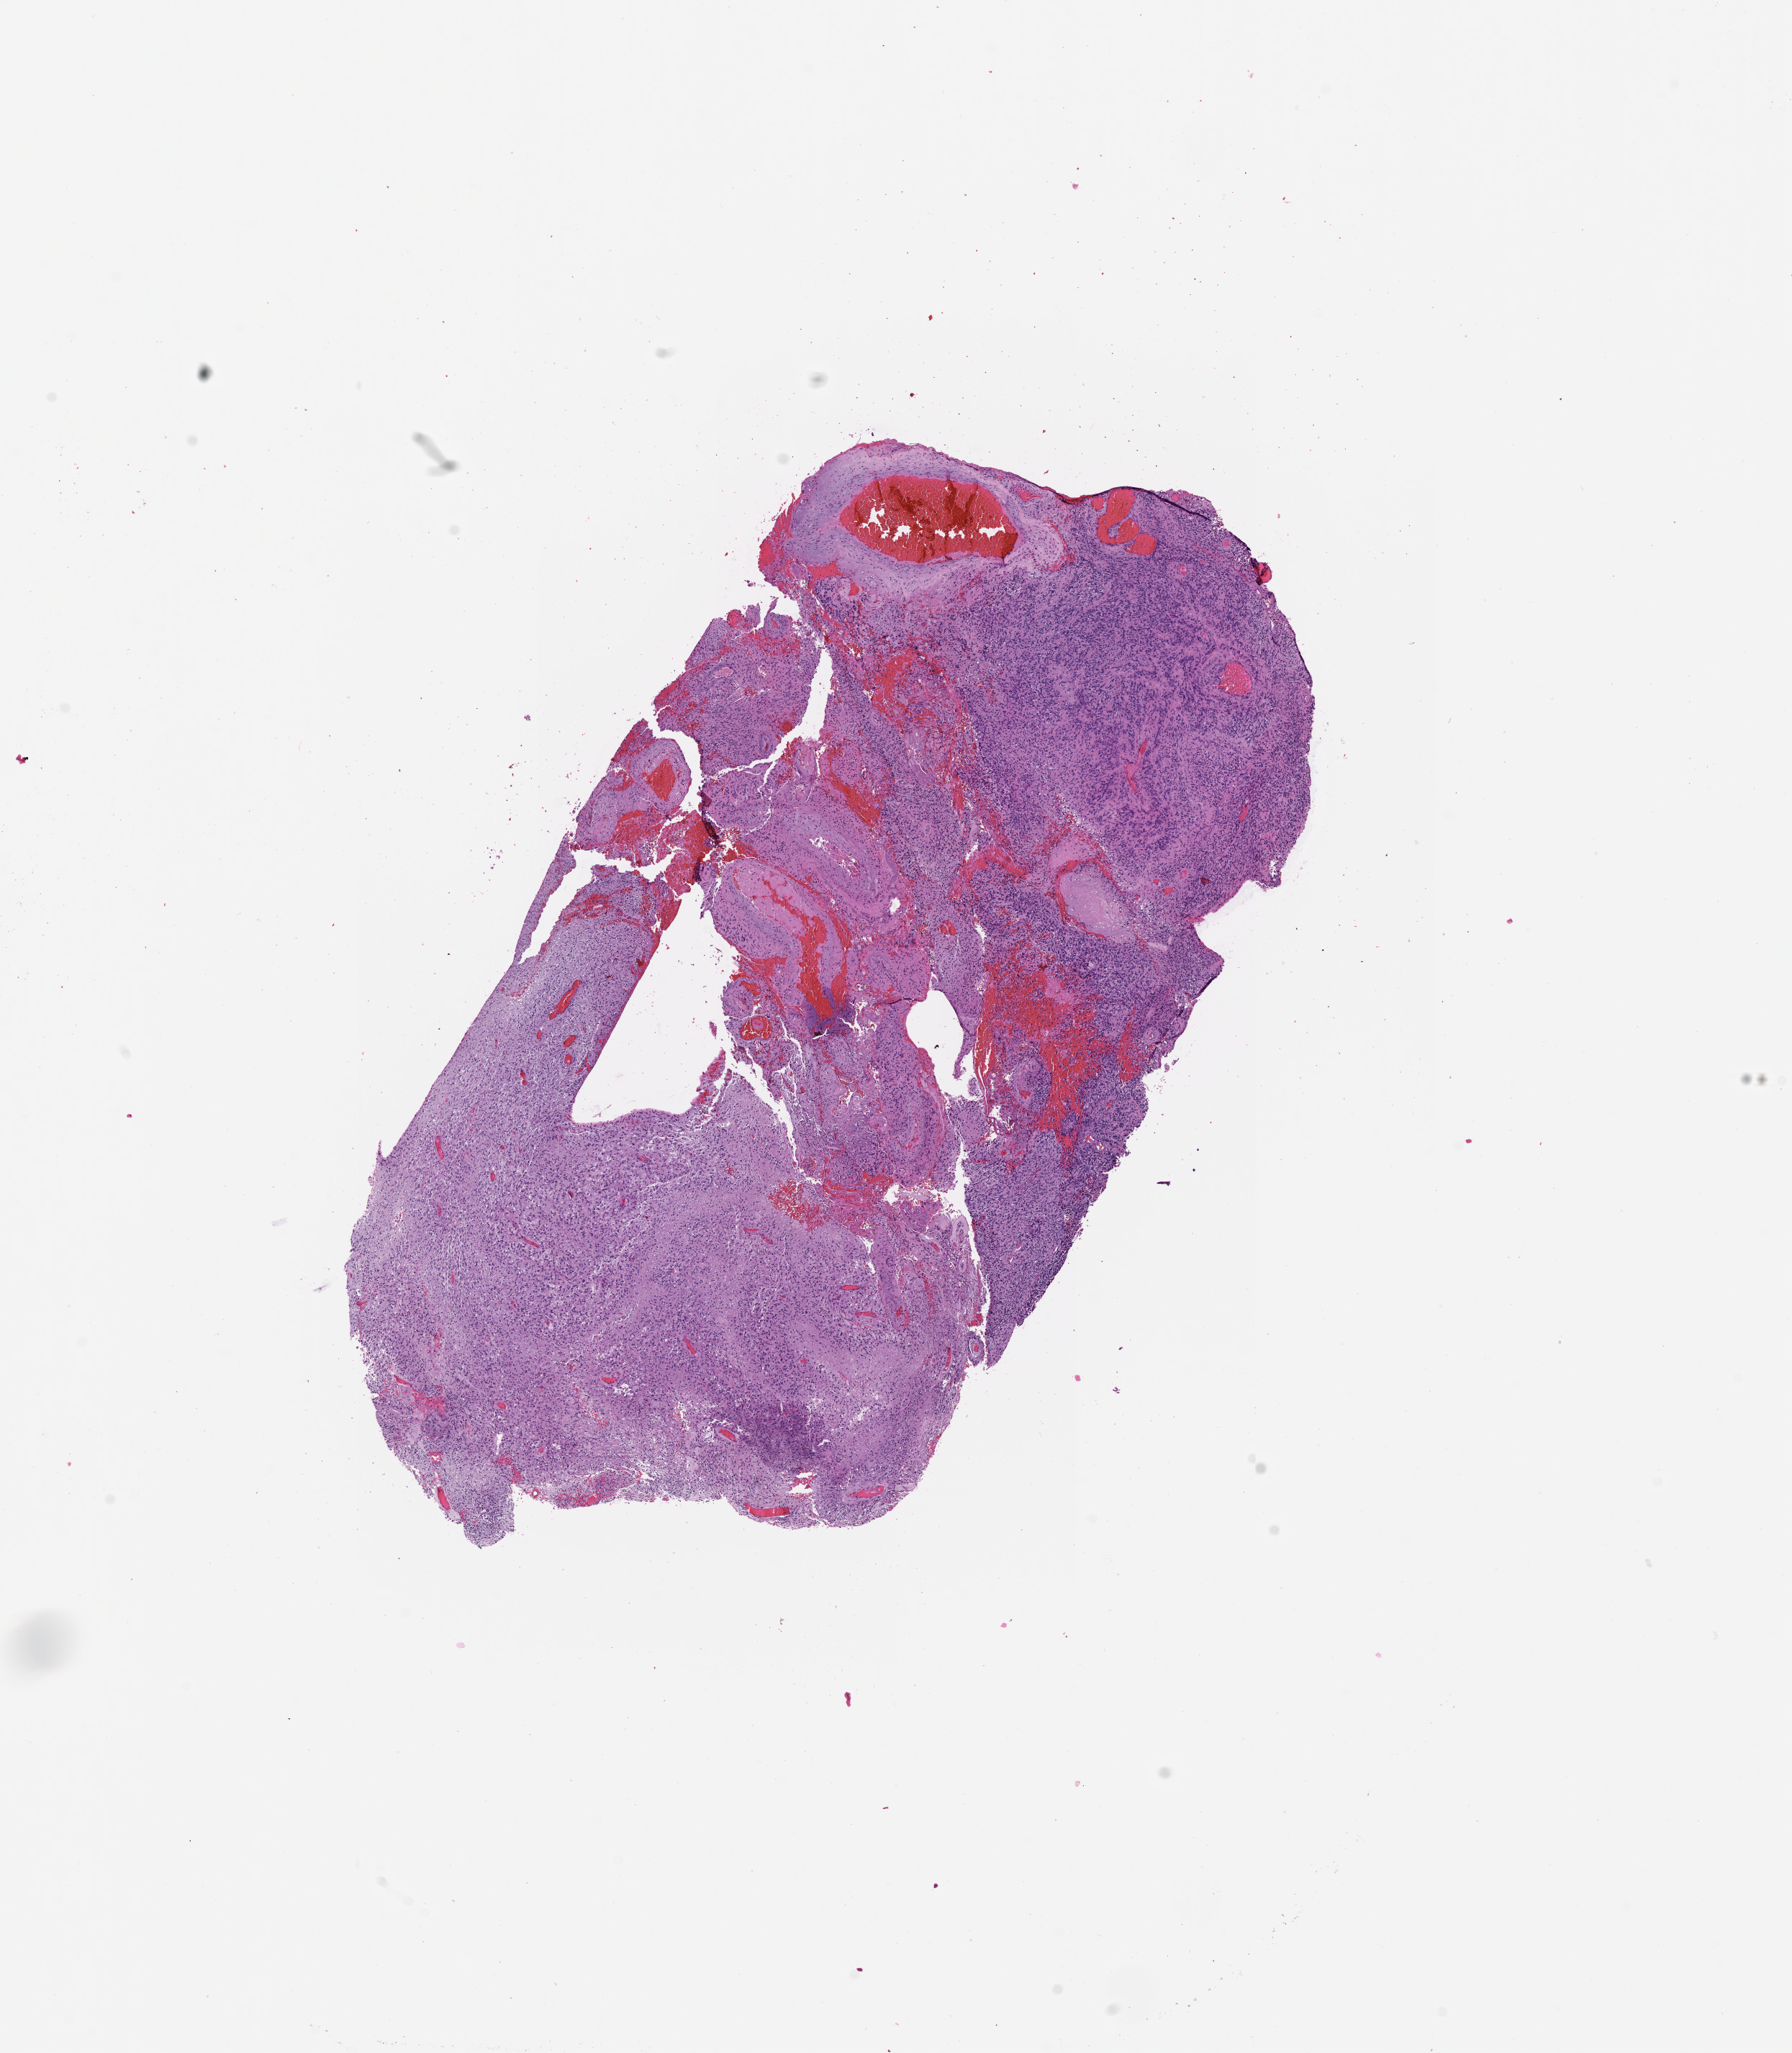
Whole-slide histology image, H&E-stained — whole scanned area (about 10.0 x 11.5 mm) shown as a low-resolution overview. Tumour tissue sample, sampled site: brain. 75-year-old male patient. Slide review estimates, as recorded: tumour nuclei 80%, necrosis 5%.
Primary tumour site (as recorded): temporal lobe. Histologic diagnosis: Glioblastoma.